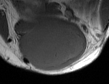
MRI of an extremity soft-tissue mass, one axial slice; slice 21 of 50 in the series (ordered by position); MR volume resampled by the dataset authors to the PET/CT grid (not the native acquisition matrix); 109 × 84 image matrix, field of view 106 × 82 mm. Male patient. Case-level facts recorded for this patient, not image findings: histological type: synovial sarcoma; site of the primary tumour: left poplietal fossa.
Structures marked on this image (expert contour drawn on MRI and transferred to this co-registered scan by the dataset authors):
- gross tumour volume (mass): bounding box [x1, y1, x2, y2] px = [16, 23, 88, 72]